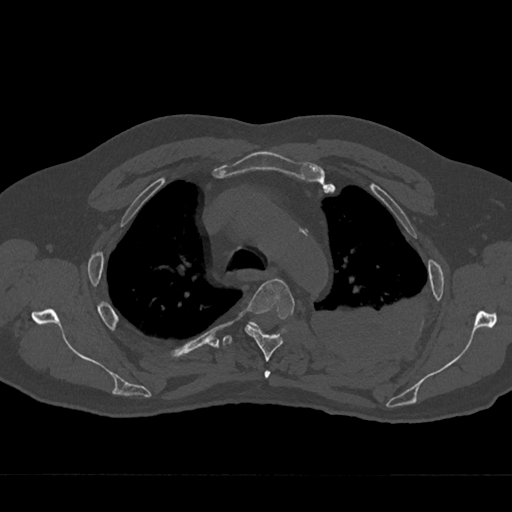
CT including the spine, one axial slice. Slice 515 of 797 in the series (ordered by position). Reconstruction kernel Br40s/3. 120 kVp. Bone window (W 1800 / L 400 HU). 0.5 mm slice thickness. 512 × 512 image matrix. Male patient, age 75 years. Case-level facts recorded for this patient, not image findings: primary cancer: renal.
Outlined on this slice (semi-automatic segmentation, software-assisted and operator-edited):
- T3 vertebra: box from (x=264, y=370) to (x=271, y=378) px
- T4 vertebra: (x=245, y=278)–(x=295, y=362)
- T5 vertebra: (x=223, y=321)–(x=260, y=346)